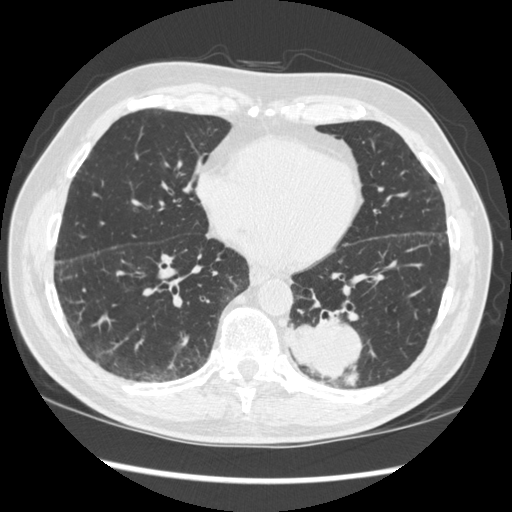
Low-dose screening chest CT, axial slice. Baseline annual screen. Lung window (W 1500 / L -600 HU). 120 kVp. Slice 122 of 348 in the series. Male participant, aged 72 years at enrolment. Current smoker at enrolment.
• Expert reader's lesion annotation, box from (x=273, y=297) to (x=377, y=385) px.
• The screening reader recorded 2 non-calcified nodules or masses ≥4 mm on this exam (left lower lobe, right middle lobe); which of them this box marks is not recorded.
• Official screen result: positive, change unspecified: nodule(s) >= 4 mm or enlarging nodule(s), mass(es), or other non-specific abnormalities suspicious for lung cancer.
• Later outcome: lung cancer diagnosed 37 days after this screen — squamous cell carcinoma, NOS, left lower lobe, stage IIIA (AJCC 6th edition), 60 mm at pathology.